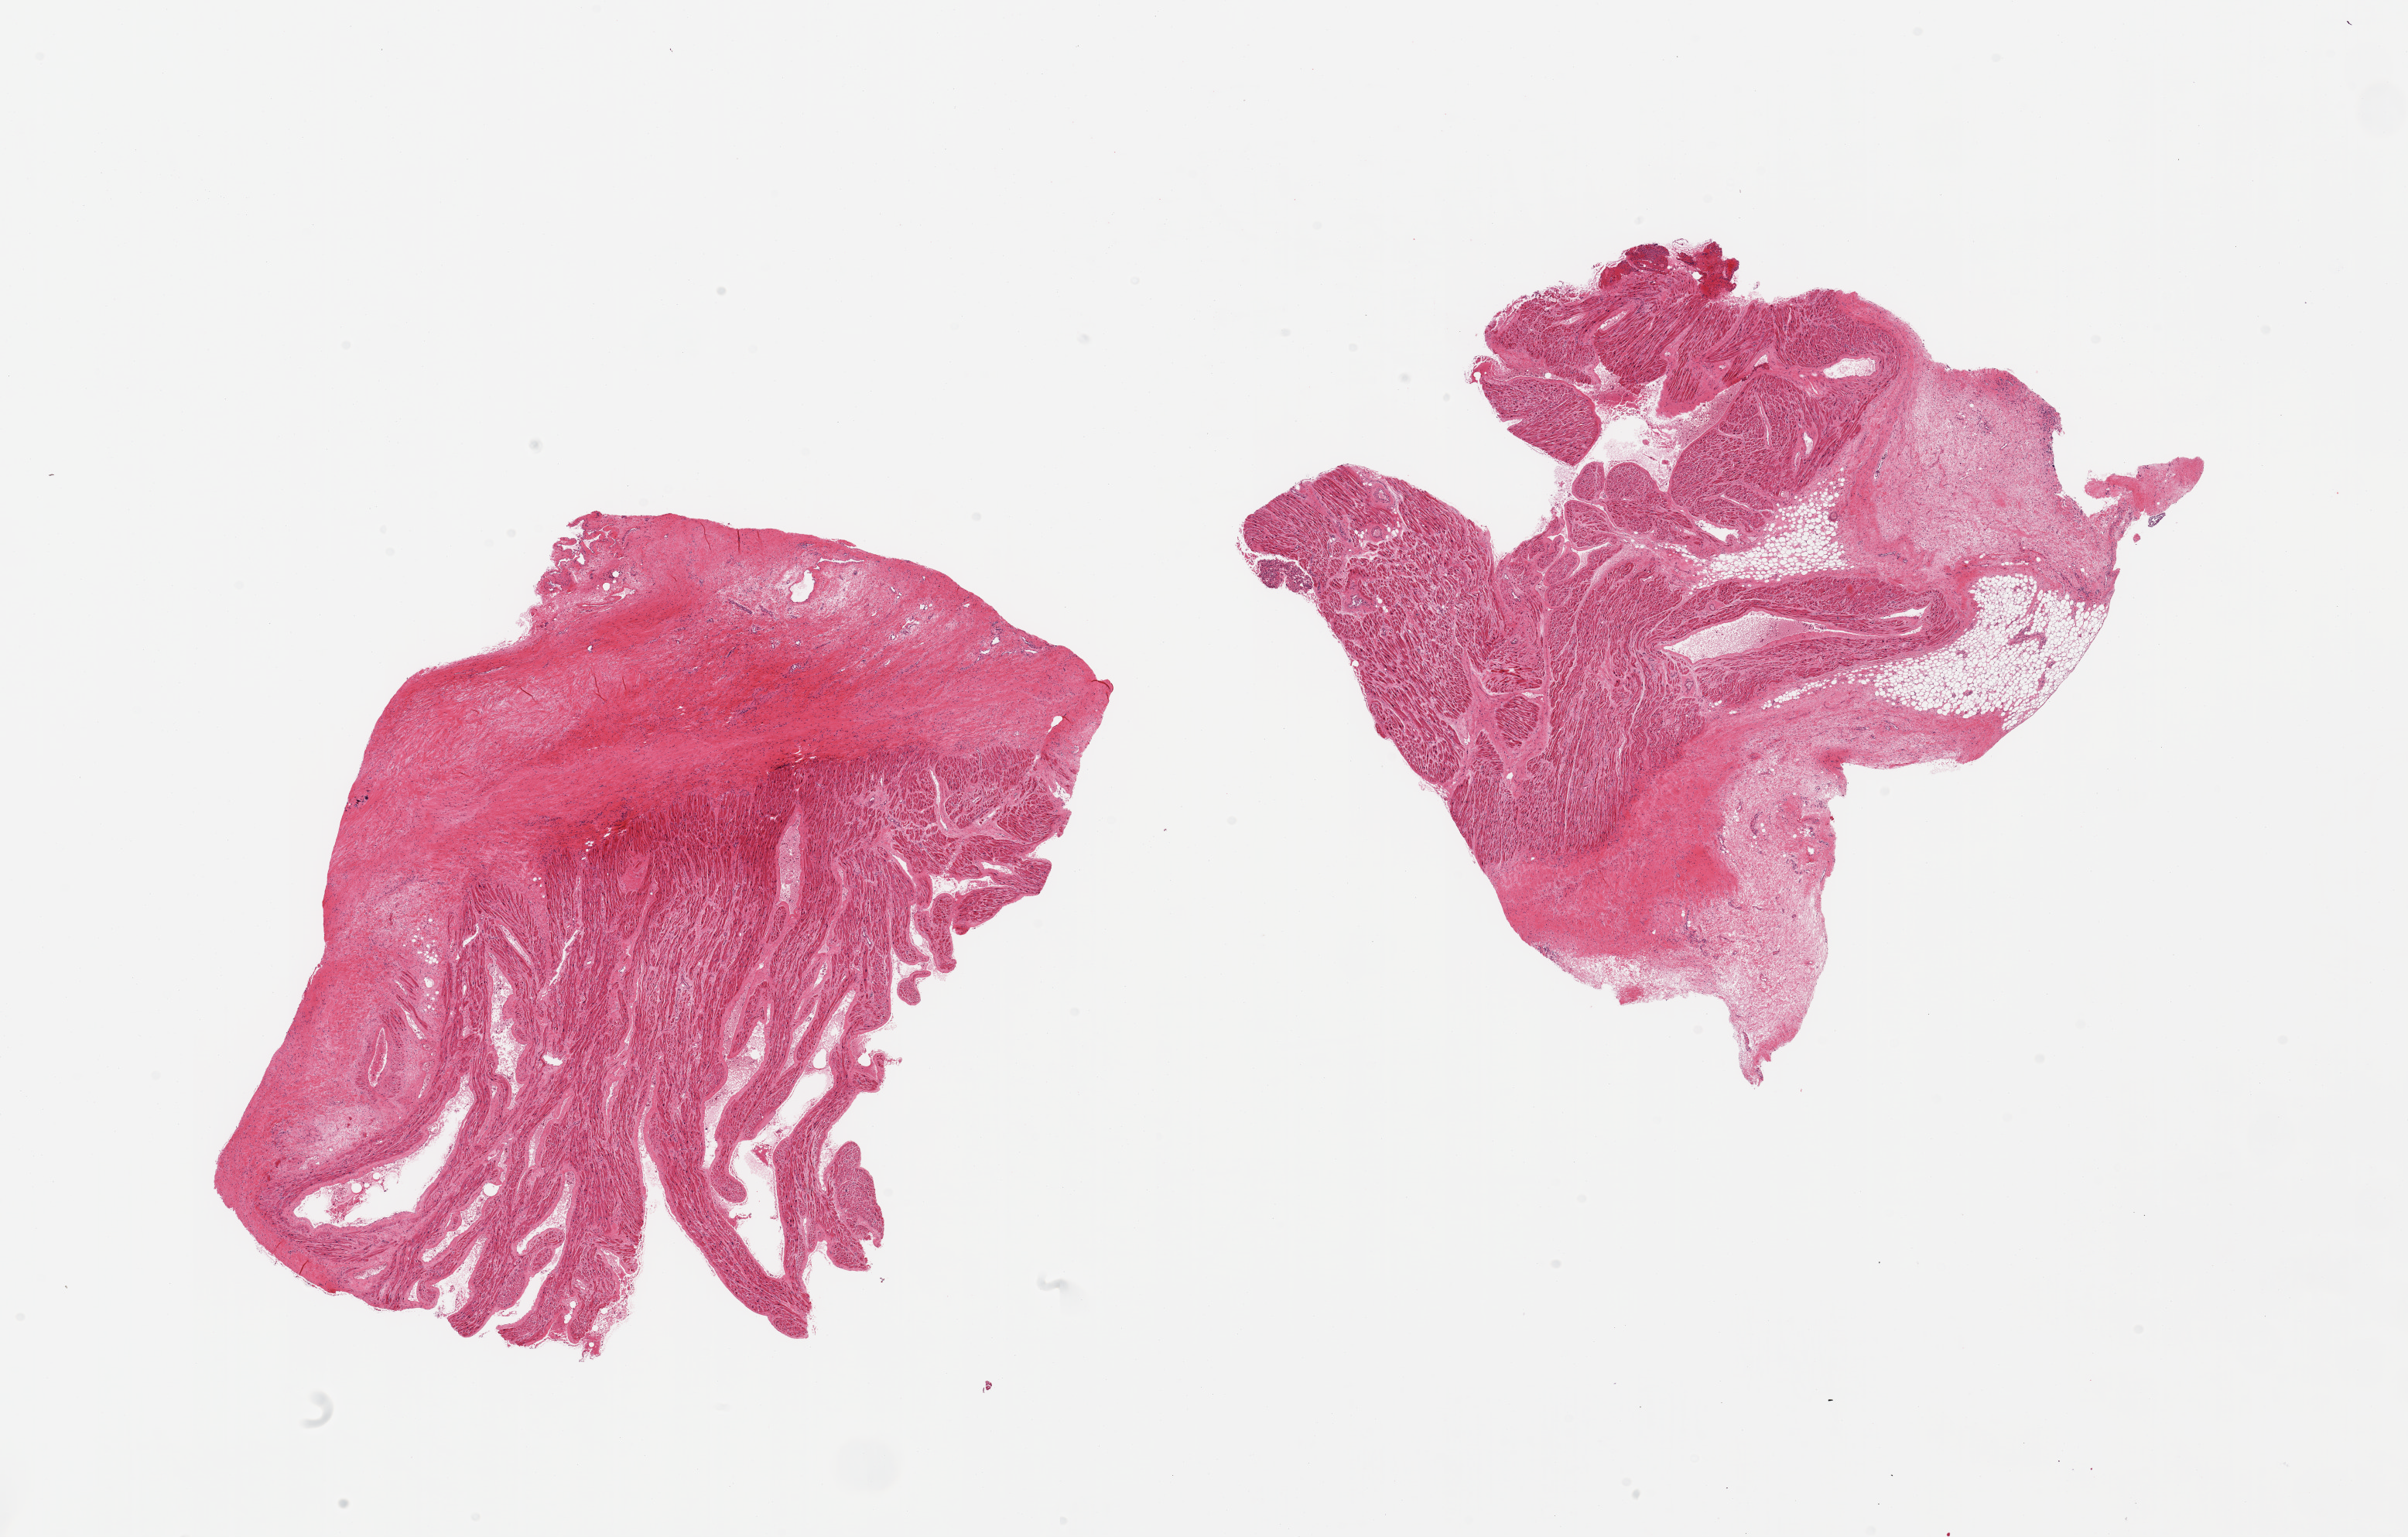
Hematoxylin and eosin (H&E) whole-slide image, shown as a low-resolution overview of the whole scanned area (about 24.6 x 15.7 mm). PAXgene-fixed paraffin-embedded (PFPE) section. Section of auricular appendage (target tissue). Donor tissue sample.
Pathologist's review note for this sample: 2 pieces; includes ~30 and 40% fat and fibrous tissue.